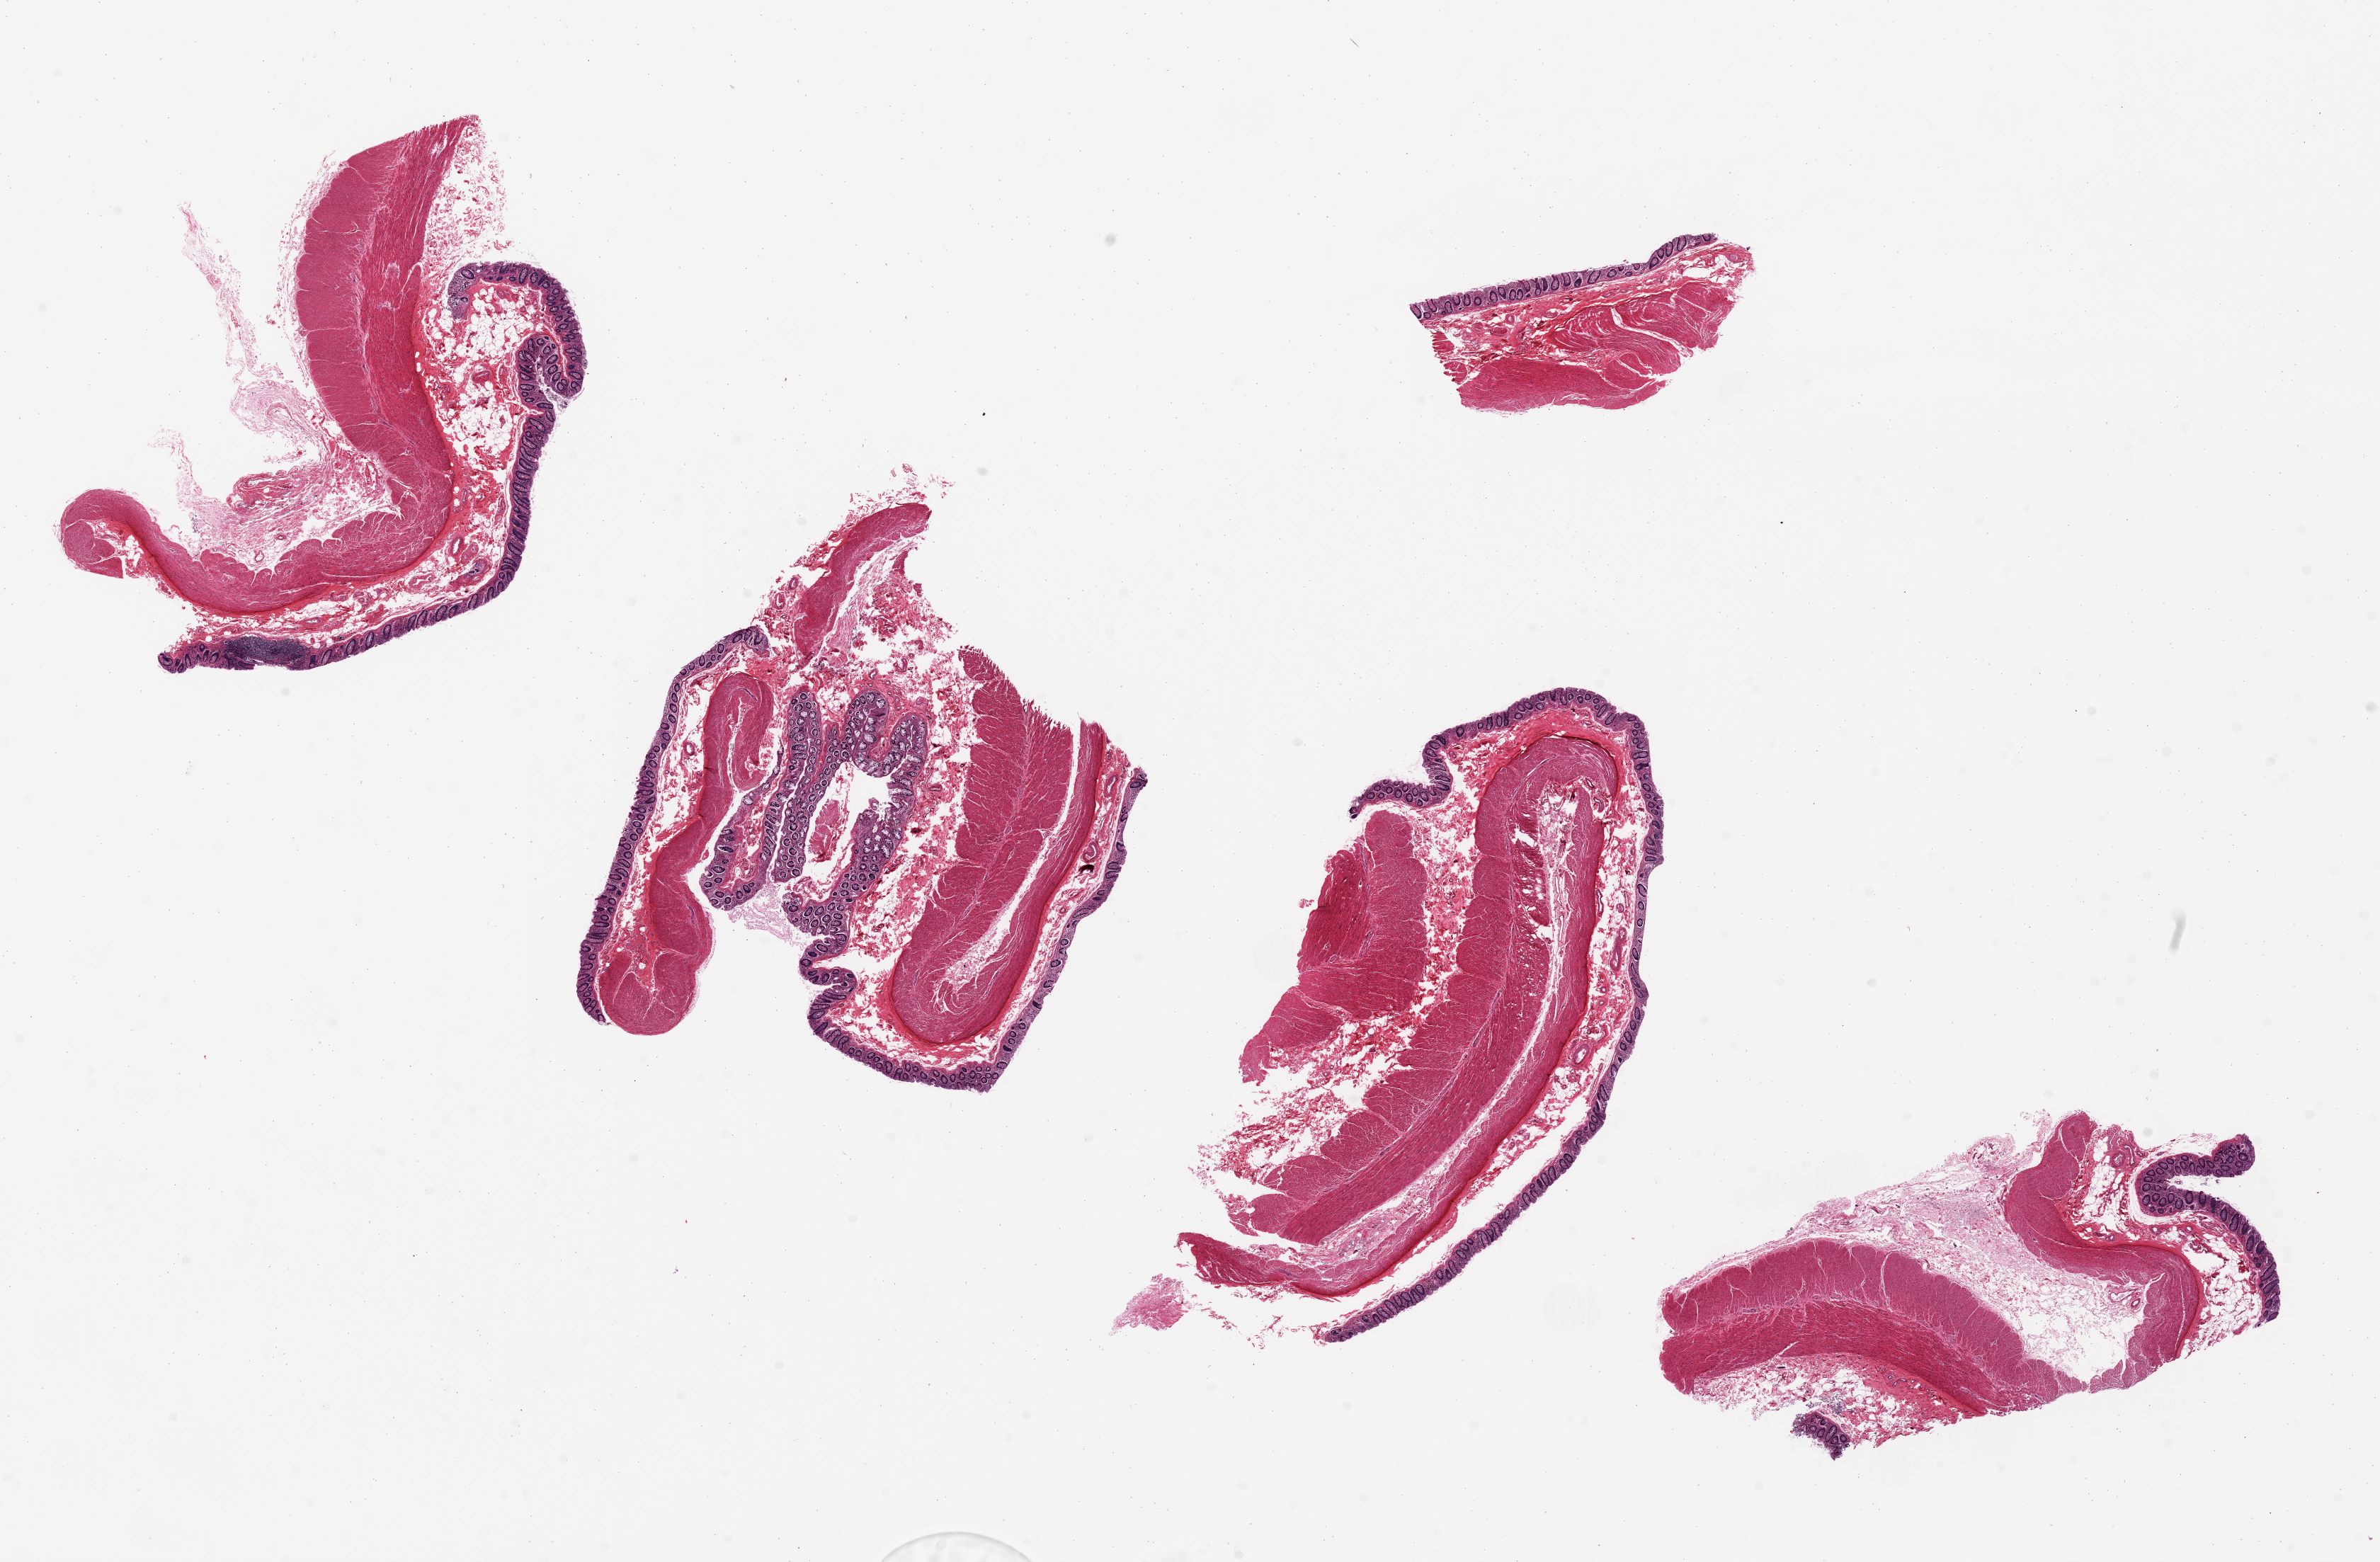
Whole-slide image, H&E stain, low-resolution overview of the scanned area, about 26.6 x 17.4 mm; PAXgene-fixed paraffin-embedded (PFPE) section; target tissue: transverse colon; donor tissue sample. Male donor.
* review note (as recorded): Much of specimen also poorly fixed (adipose portions???separation and fragmenting of sections. Mucosal thickness averages 150-200 microns, ~ 10% specimen thicknesss